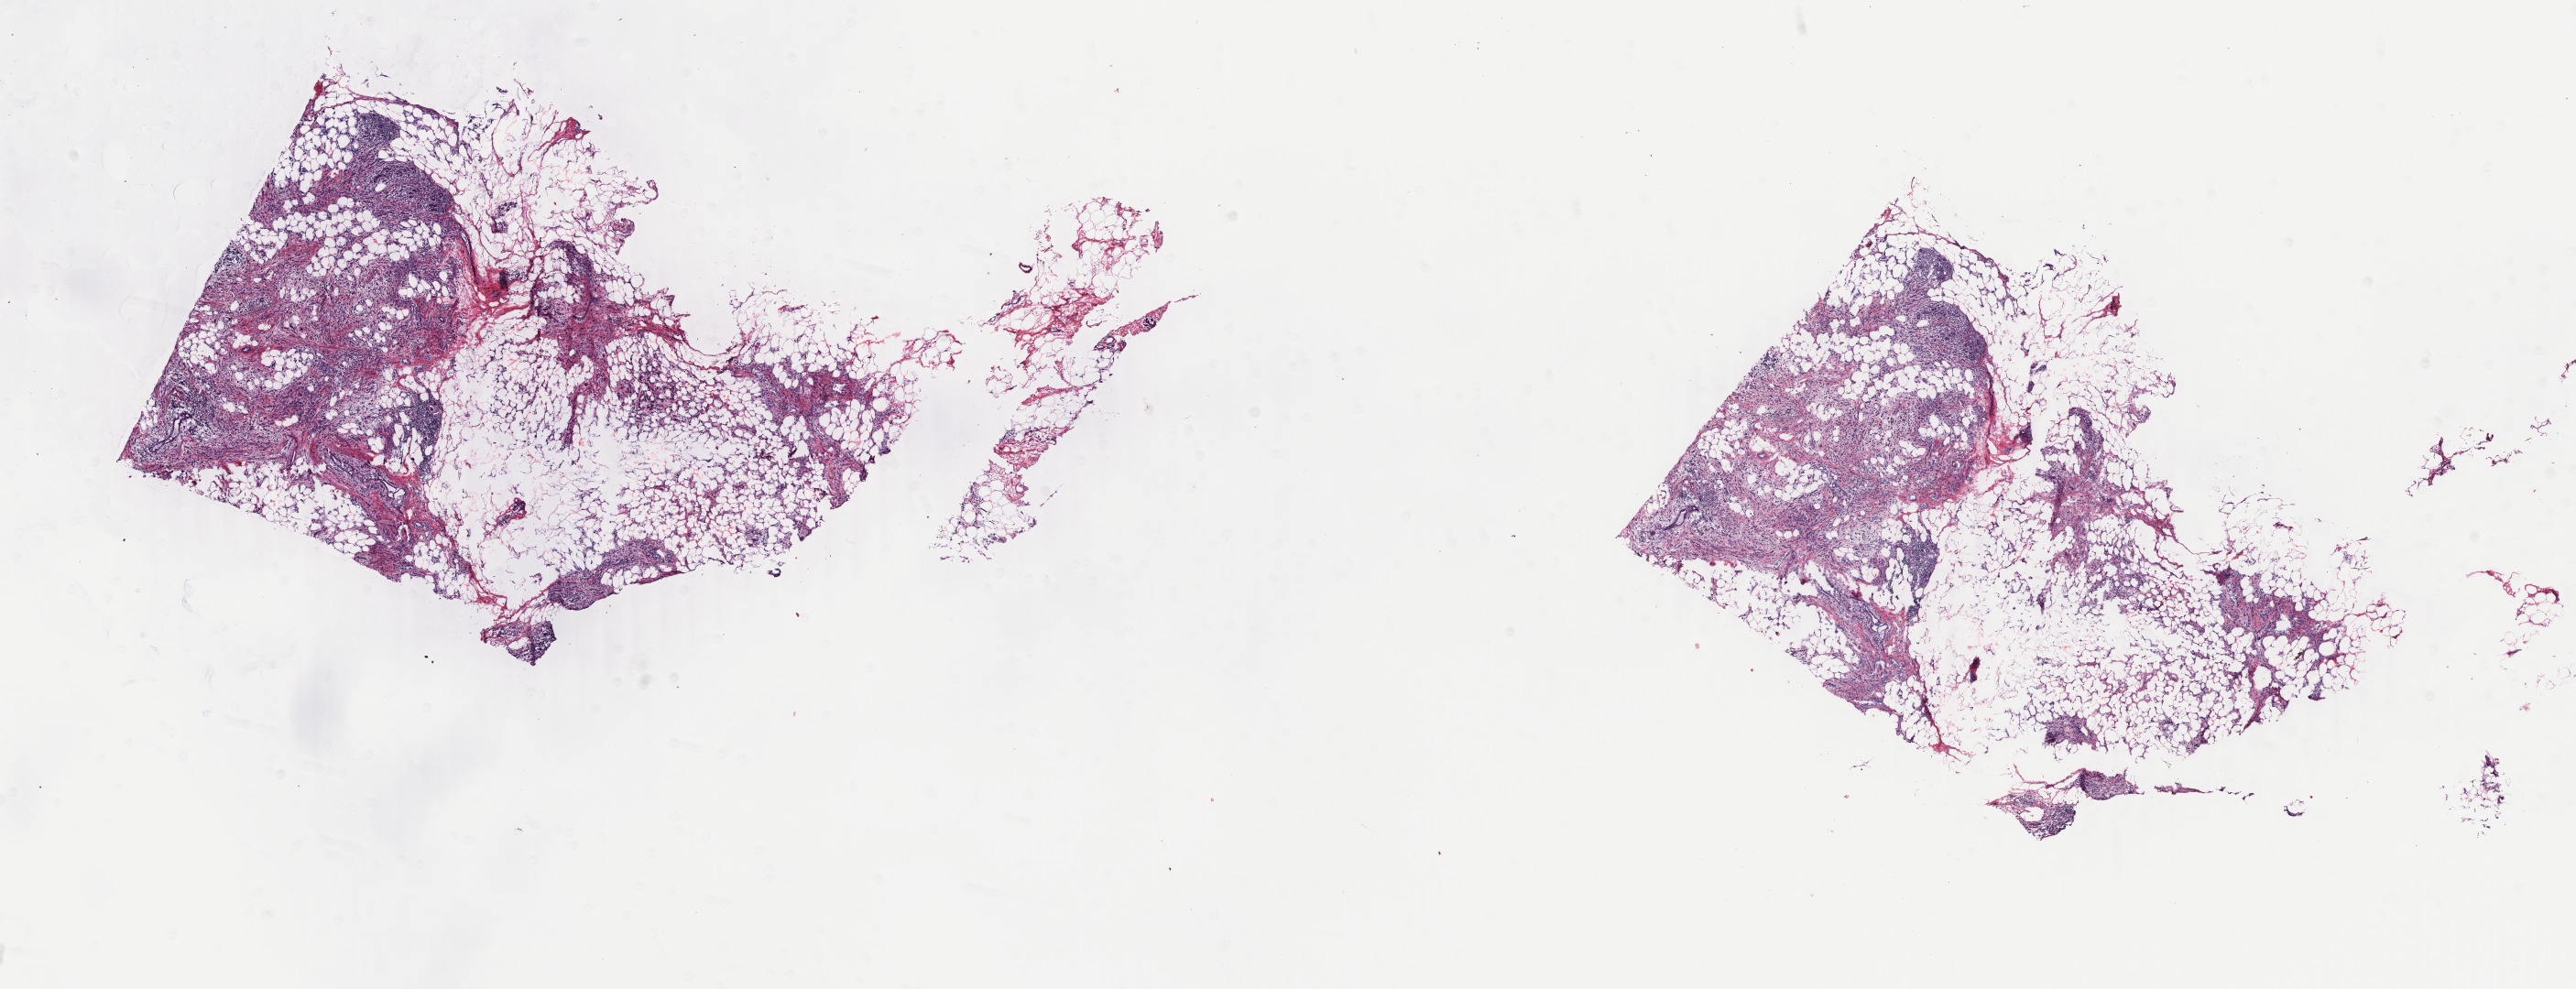
Whole-slide histology image, H&E — whole scanned area (about 22.4 x 8.6 mm, slide scanned at 40x) shown as a low-resolution overview, frozen section, sample: primary tumour, breast. Female, age 54 years at initial diagnosis. Slide review estimates, as recorded: tumour cells 80%, tumour nuclei 75%, normal cells 0%, stromal cells 20%, necrosis 0%. Inflammatory infiltration, as recorded: lymphocyte infiltration 0%, monocyte infiltration 0%, neutrophil infiltration 0%.
• lymph nodes positive (case pathology): 2 of 44 examined
• diagnosis: Lobular carcinoma, NOS
• TNM: T2 N1a M0
• AJCC pathologic stage: IIB